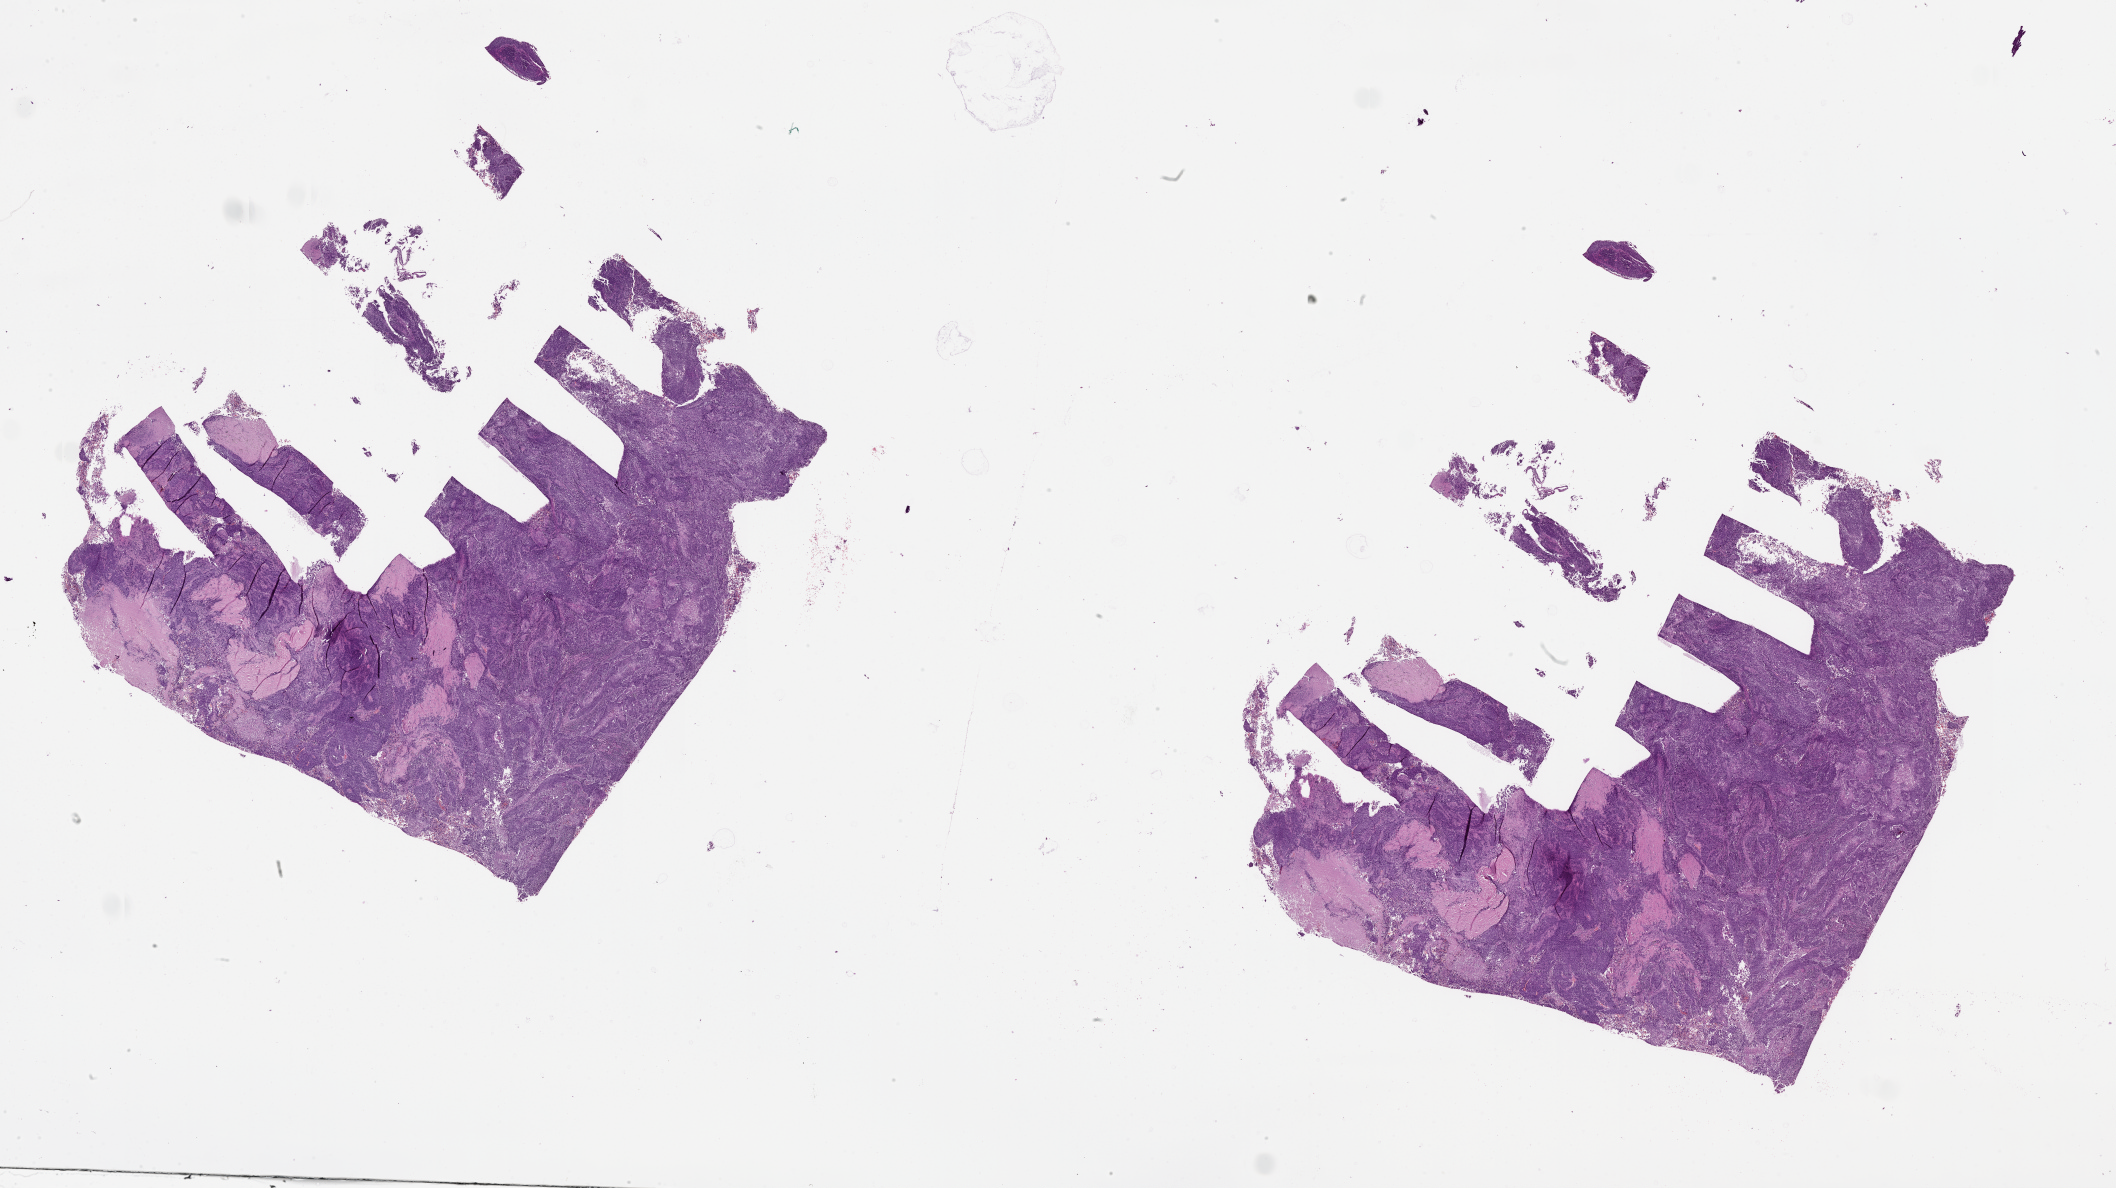
Hematoxylin and eosin (H&E) stained whole-slide image, whole scanned area (about 34.1 x 19.1 mm) shown as a low-resolution overview; lung, tumour tissue. 53-year-old male patient.
Patient diagnosis (cohort enrolment): squamous cell carcinoma (lung).